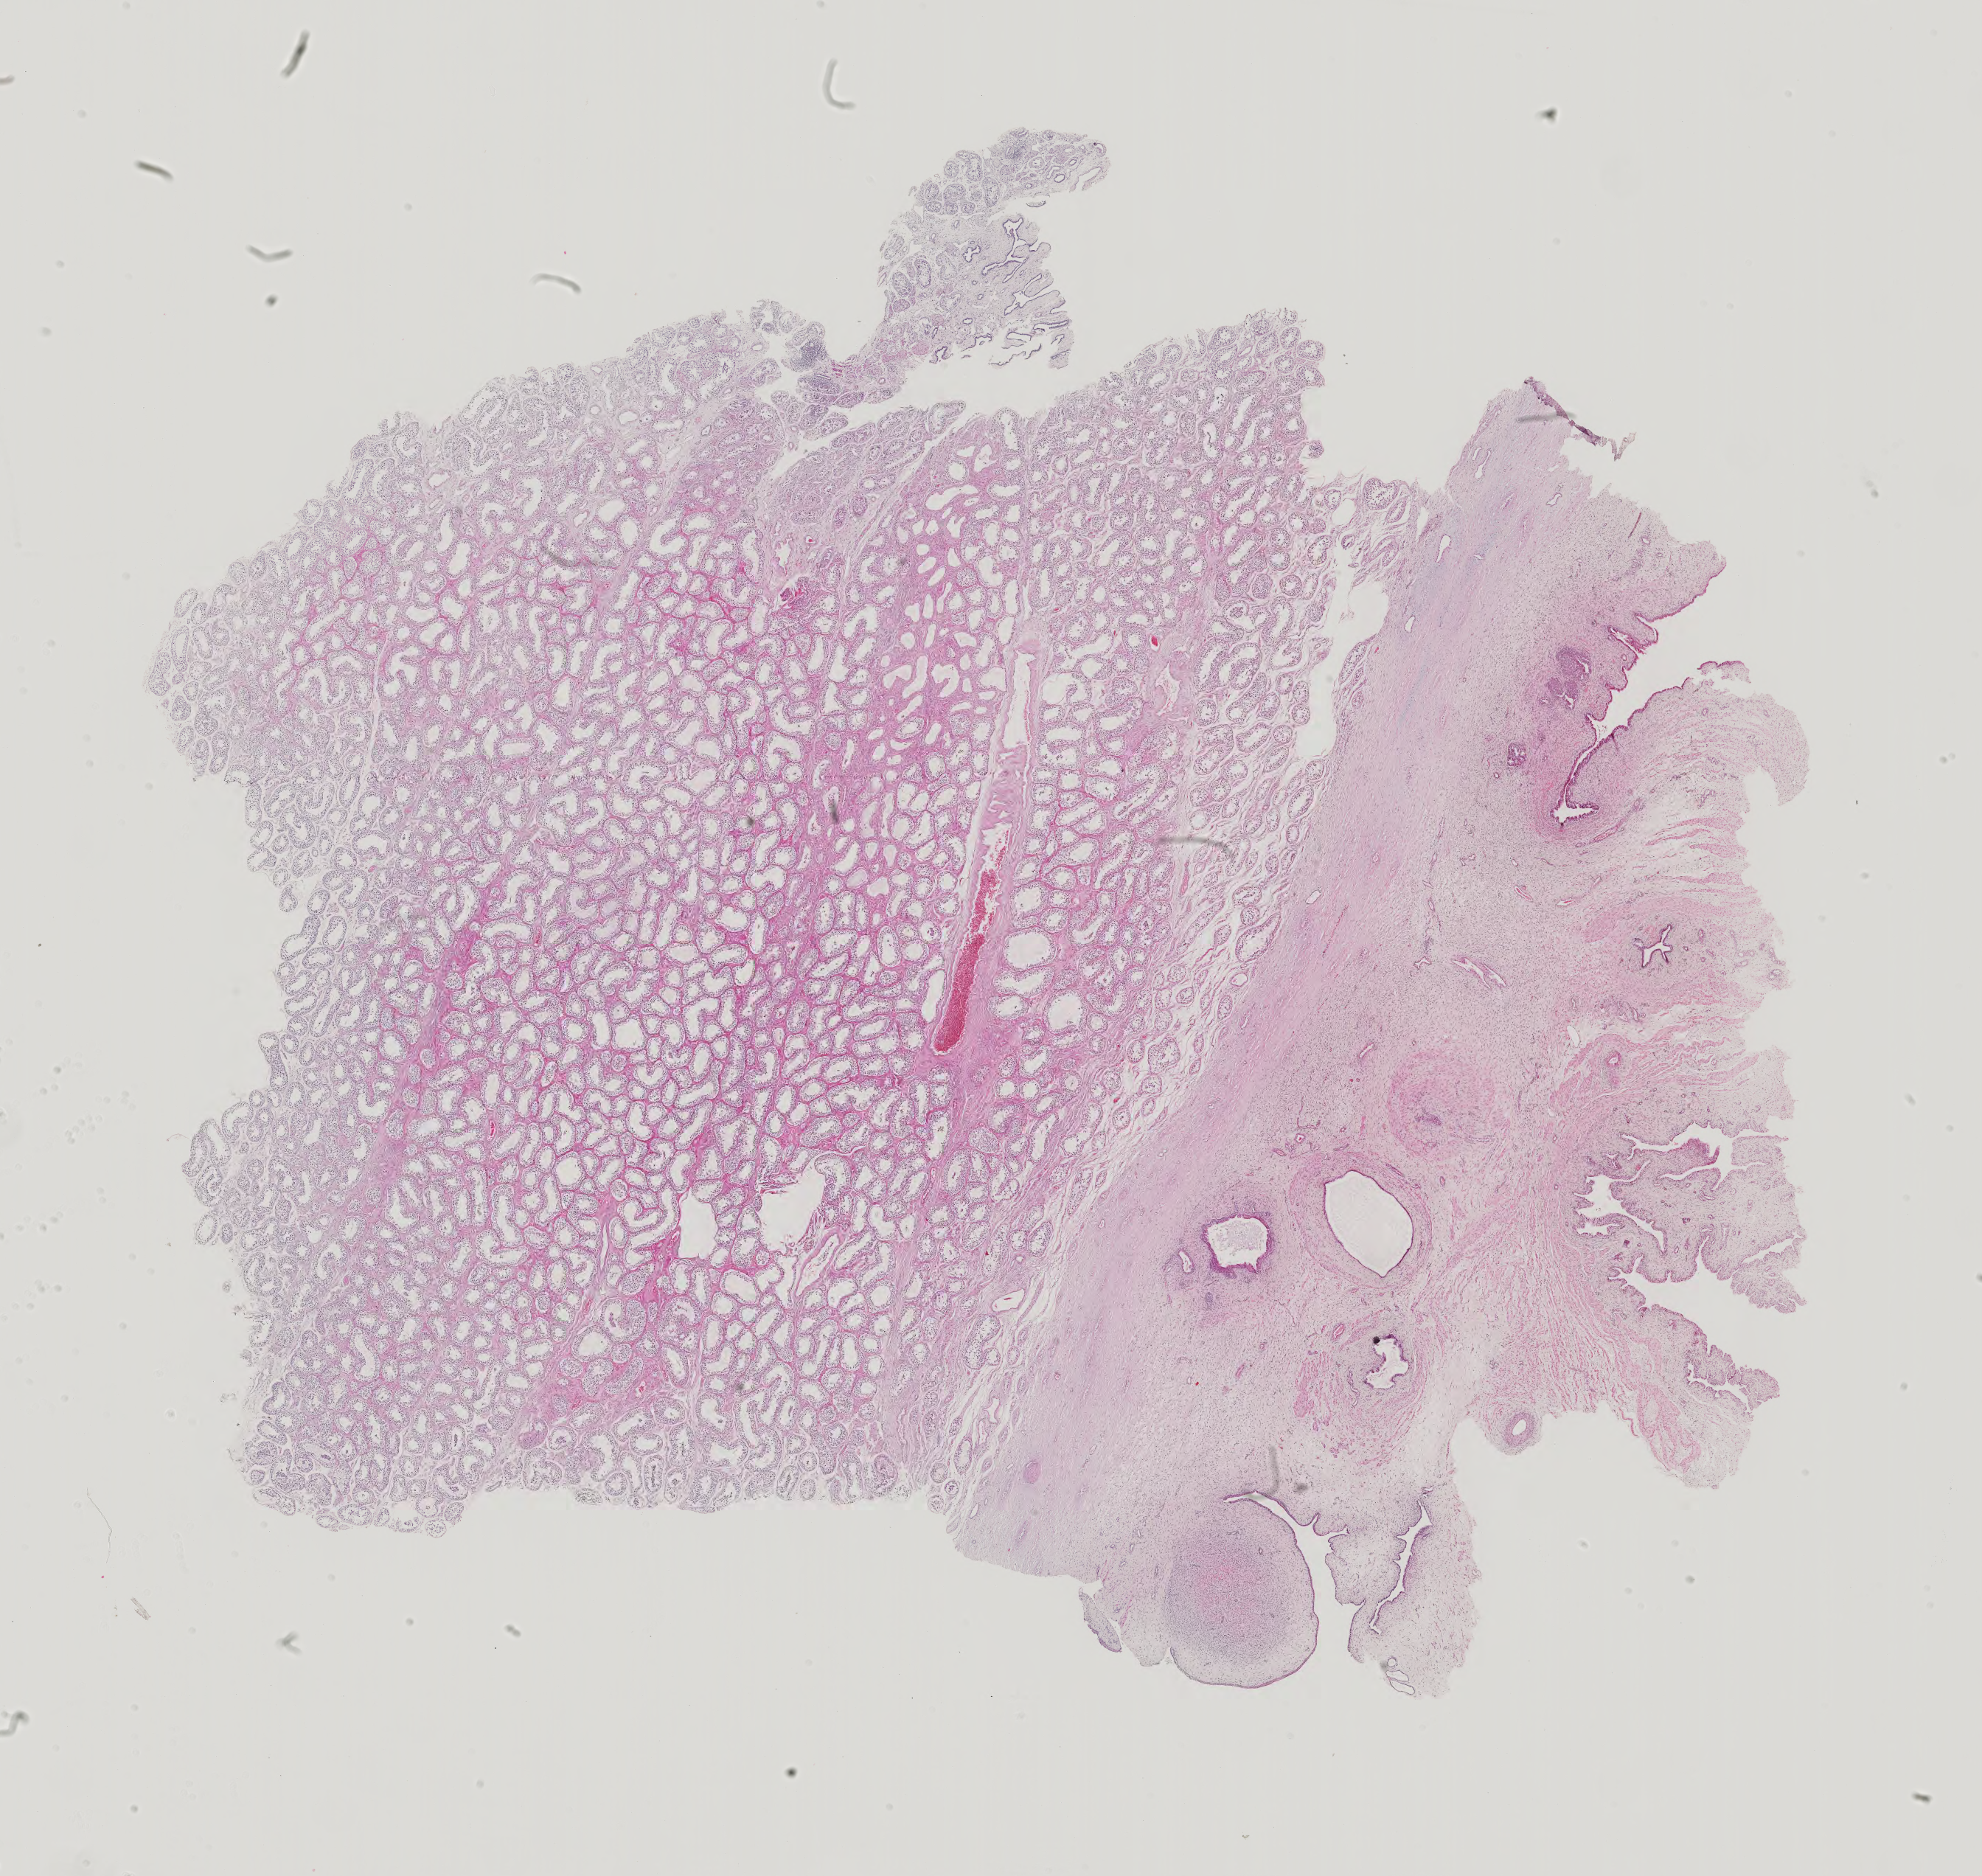
Whole-slide histology image, Hematoxylin and eosin (H&E) stained — low-resolution overview of the scanned area, about 19.6 x 18.5 mm (slide scanned at 40x); formalin-fixed paraffin-embedded (FFPE) diagnostic section; primary tumour sample from the testis. Patient: male, age at initial diagnosis 23 years.
Laterality: left. TNM: T1 NX M0. Pathologic diagnosis: Teratoma, benign. AJCC pathologic stage: II (5th edition).